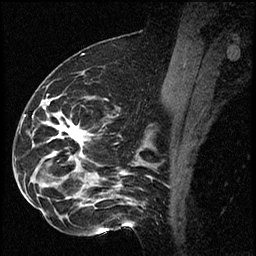
Breast MRI (dynamic contrast-enhanced), one sagittal slice; position 36 of 60 along the scan axis; dynamic contrast-enhanced series, image 2 of 2 at this slice position (ordered by acquisition); 1.5 T; TE 4.2 ms, TR 17.3 ms; 256 × 256 image matrix, field of view 200 × 200 mm. Female patient. Case-level facts recorded for this patient, not image findings: setting: breast cancer imaged before/during neoadjuvant chemotherapy; receptor status: HR-positive, HER2-negative.
Annotated regions visible in this slice (semi-automatic segmentation, software-assisted and operator-edited):
- analysis volume of interest (the breast-tissue region the enhancement analysis was run in; not a lesion): bounding box (x1, y1, x2, y2) in pixels: (41, 97, 115, 223)
- tumour enhancement mask (voxels above the 100 % enhancement threshold inside the analysis volume of interest): (59, 126, 84, 145)